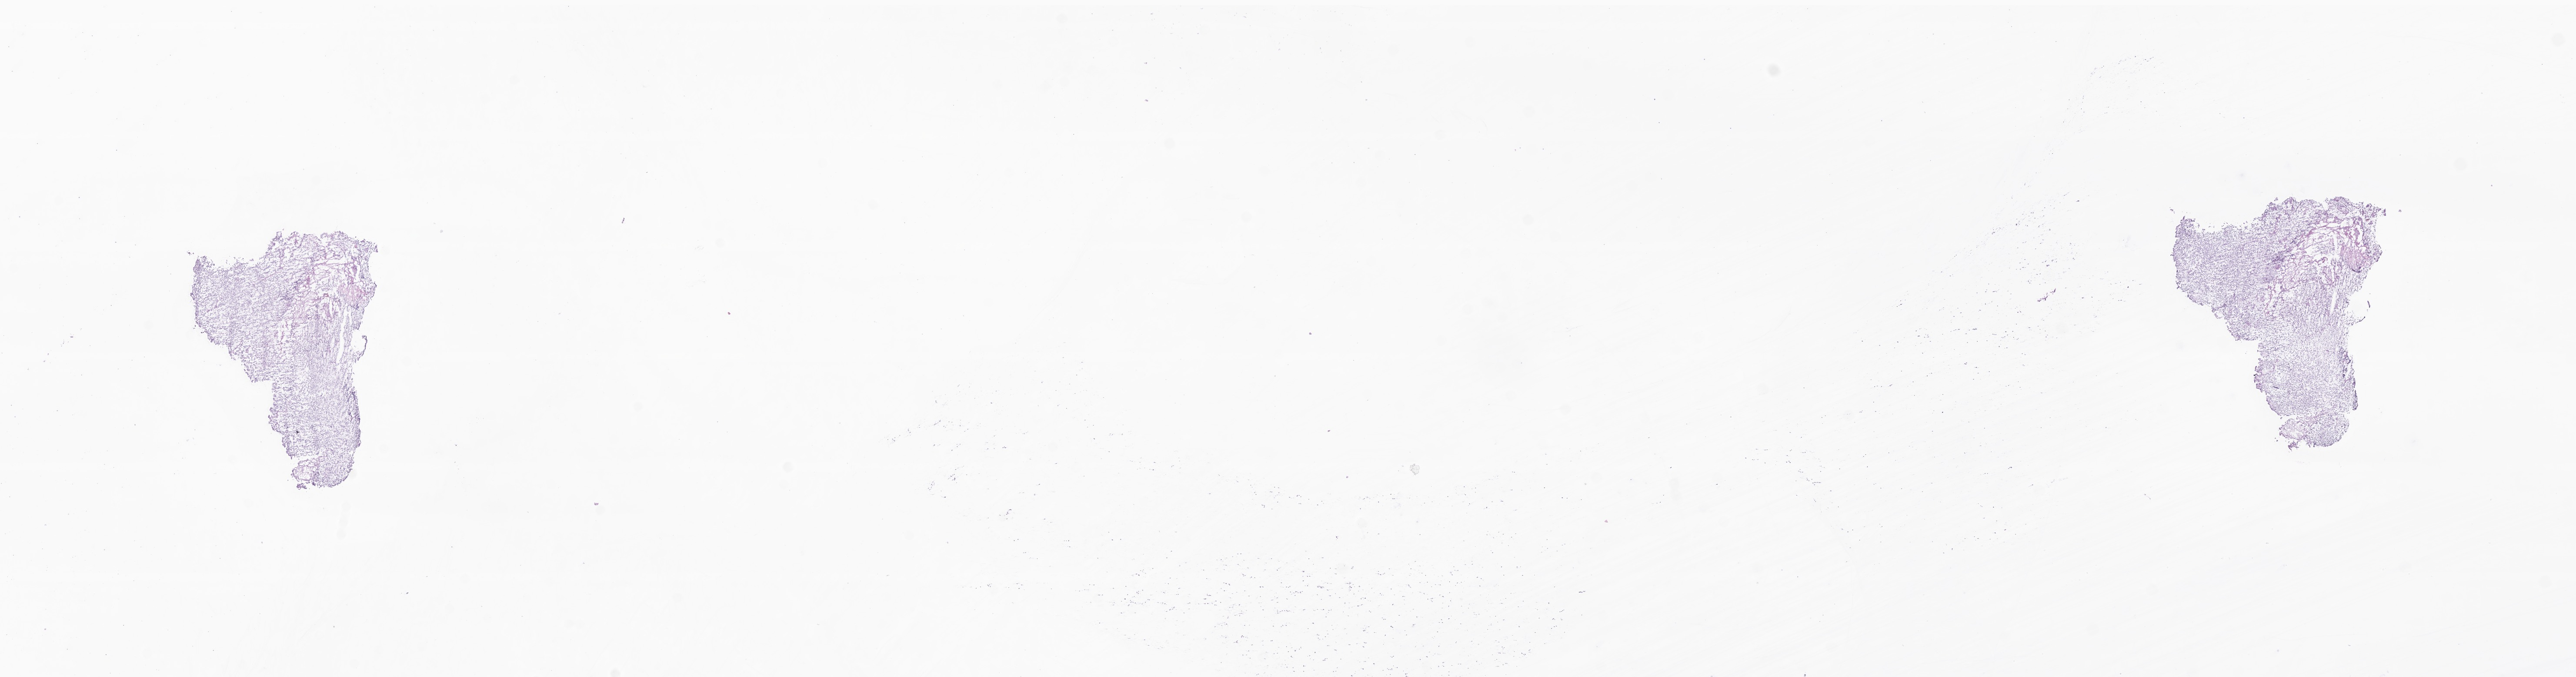
H&E whole-slide image of tumor tissue from the brain, low-resolution overview of the scanned area, about 25.0 x 6.6 mm; frozen section (OCT-embedded). Male patient, age 47 months (3 years 11 months).
Diagnosis (ICD-O-3 morphology term): Medulloblastoma, NOS.